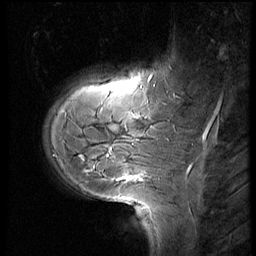
Breast MRI (dynamic contrast-enhanced), one sagittal slice; position 14 of 60 along the scan axis; 3 images stored at this slice position (order not interpretable as contrast timing); 1.5 T; TE 4.2 ms, TR 8.9 ms; 2.5 mm slice thickness; 256 × 256 image matrix, field of view 200 × 200 mm. Patient: female, 29 years. Case-level facts recorded for this patient, not image findings: setting: breast cancer imaged before/during neoadjuvant chemotherapy.
Outlined on this slice (semi-automatically segmented with operator editing):
- analysis volume of interest (the breast-tissue region the enhancement analysis was run in; not a lesion): bounding box <45,57,185,200> (left, top, right, bottom; pixels)
- tumour enhancement mask (voxels above the 140 % enhancement threshold inside the analysis volume of interest): <108,151,141,180>